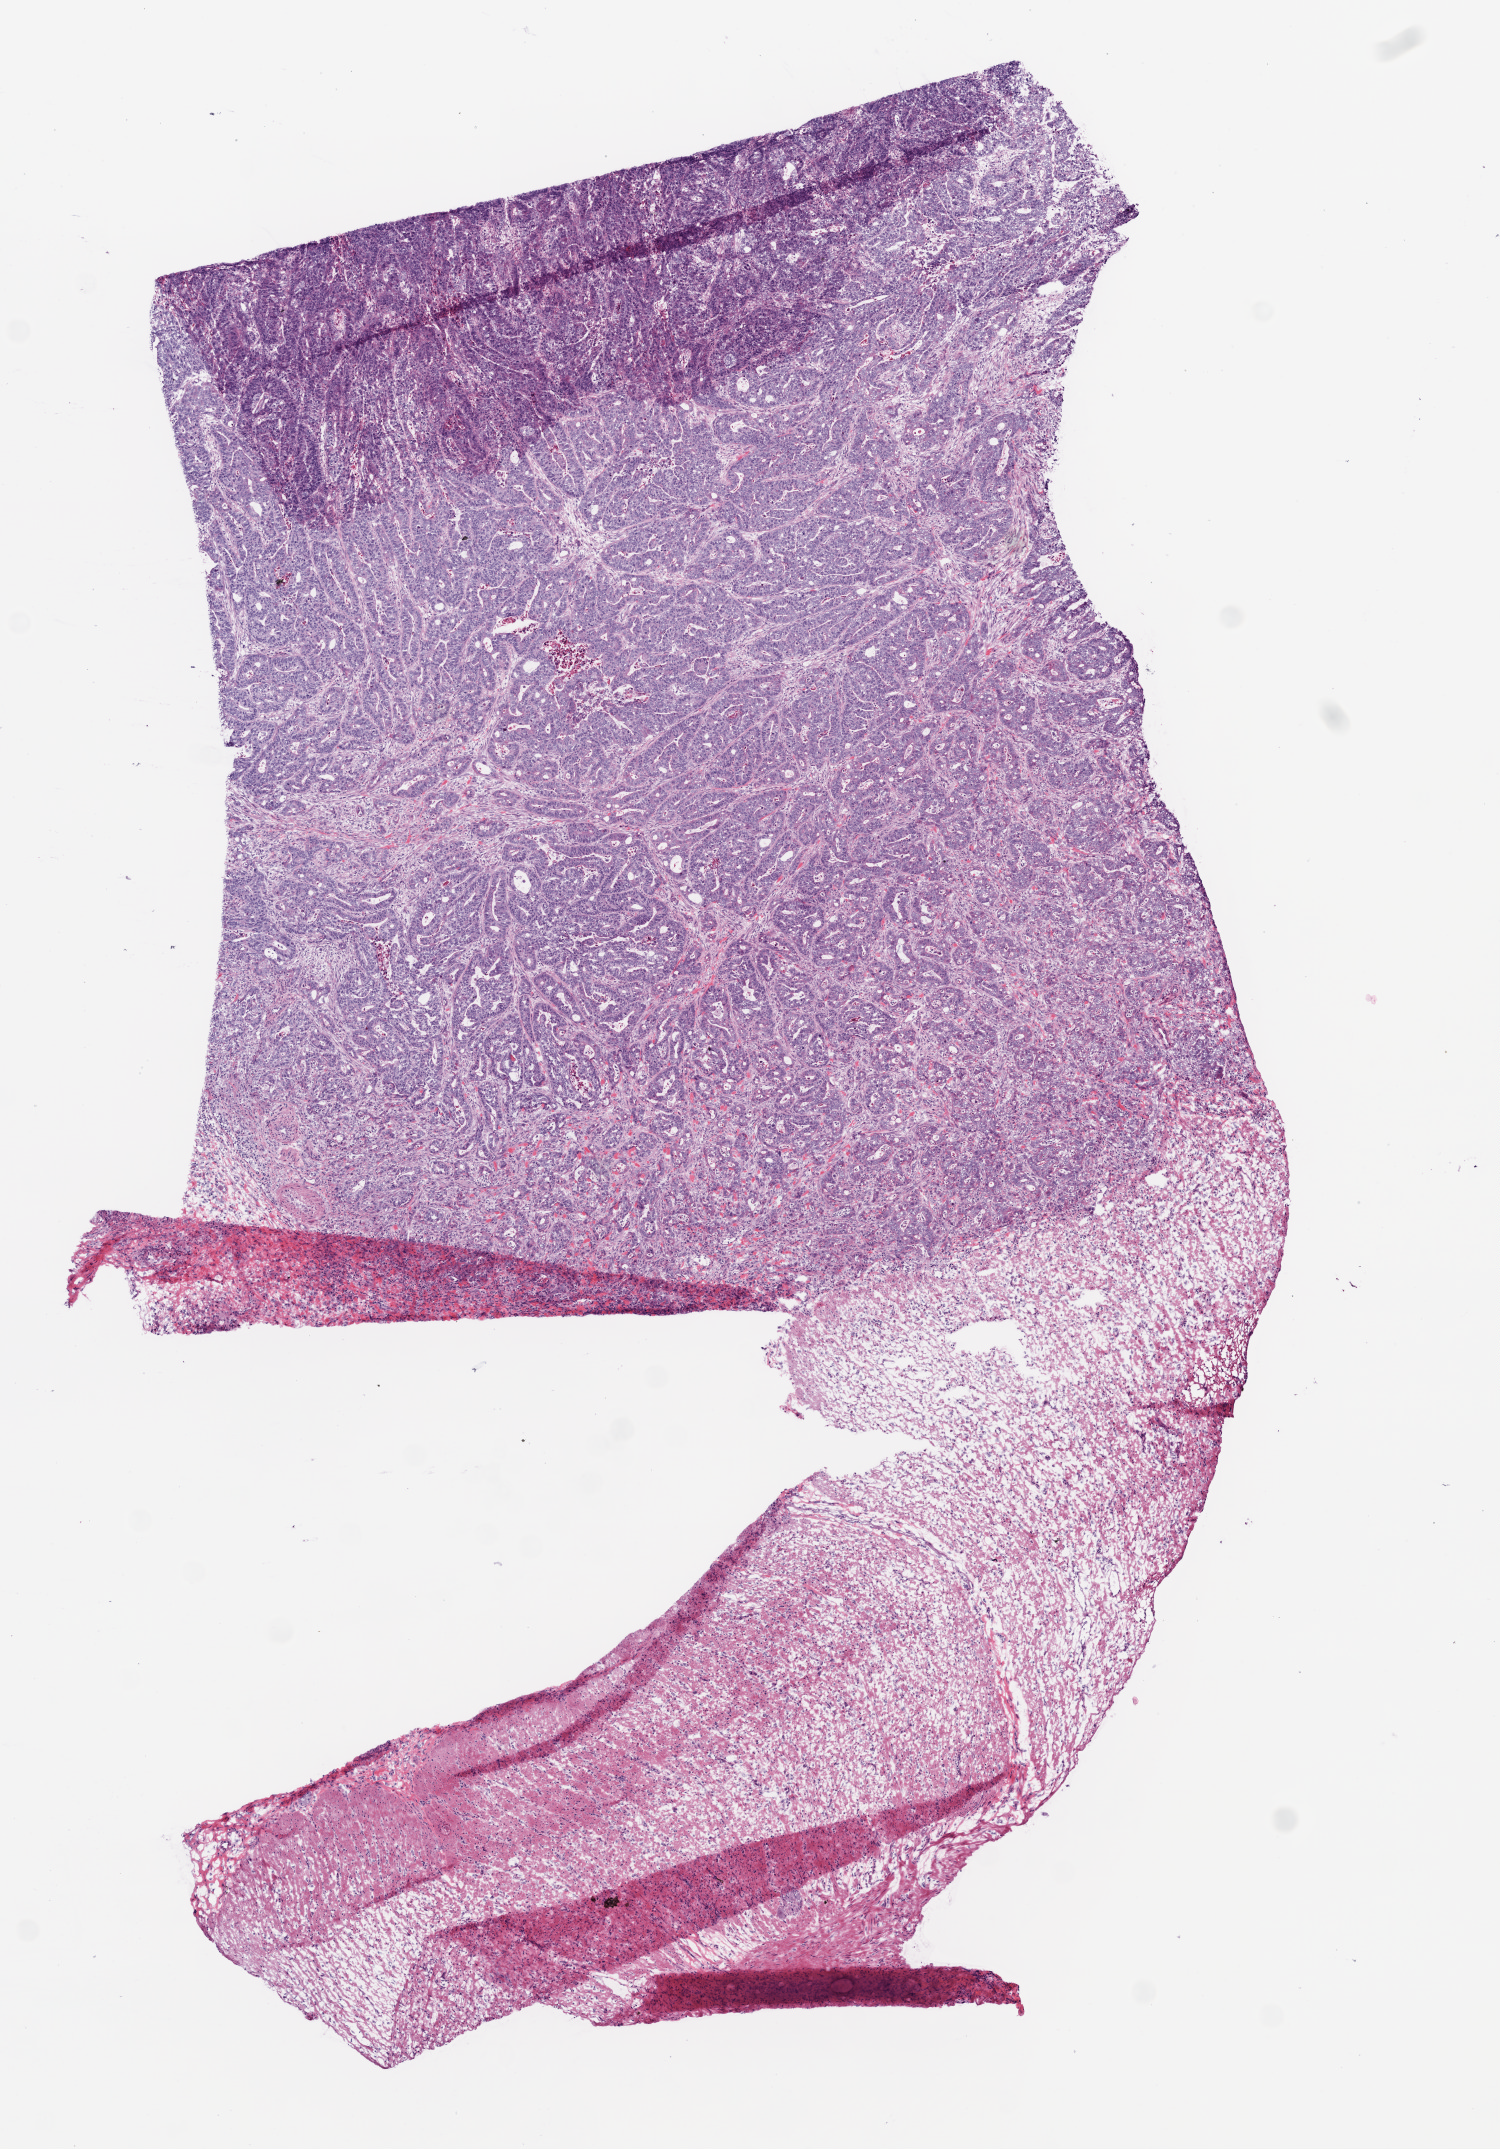
Digitized H&E-stained tissue section (whole slide) — shown as a low-resolution overview of the whole scanned area (about 6.0 x 8.6 mm, from a 20x scan). Frozen section from the bottom of the tissue portion. Rectum, primary tumour sample. Patient: male, age at initial diagnosis 64 years. Pathologist review of this section (percent, as recorded): tumour cells 60%, tumour nuclei 80%, normal cells 30%, stromal cells 5%, necrosis 5%.
- histologic diagnosis: Adenocarcinoma, NOS
- lymph nodes positive (case pathology): 7 of 40 examined
- AJCC pathologic stage: IV (6th edition)